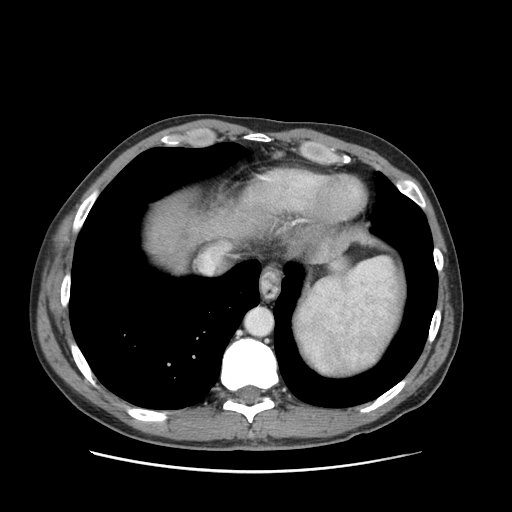
Contrast-enhanced abdominal CT (liver protocol), one axial slice. Position 84 of 93 along the scan axis. Reconstruction kernel STANDARD. Soft-tissue window (W 400 / L 40 HU). 2.5 mm slice thickness. 512 × 512 image matrix. From the clinical record (not read from this slice): diagnosis: hepatocellular carcinoma (patient treated with transarterial chemoembolisation; whether this scan precedes or follows treatment is not stated here); TNM stage (as recorded): Stage-II; Child-Pugh class: A; tumour differentiation: moderately differentiated; tumour size: 1 cm.
Structures marked on this image (semi-automatically segmented with operator editing):
- abdominal aorta: bounding box (x1, y1, x2, y2) in pixels: (245, 308, 272, 336)
- liver parenchyma outside the tumour (the mass and vessels are separate outlines, so this box may not span the whole liver): (148, 196, 246, 270)